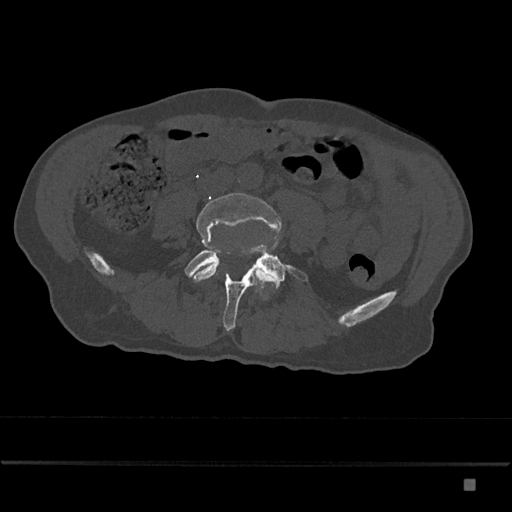
CT including the spine, one axial slice. Position 304 of 797 along the scan axis. Reconstruction kernel Br40s/3. Bone window (W 1800 / L 400 HU). 0.5 mm slice thickness. 512 × 512 image matrix, field of view 390 × 390 mm. Male patient, age 72 years. From the clinical record (not read from this slice): primary cancer: prostate.
Structures marked on this image (semi-automatically segmented with operator editing):
- L4 vertebra: bounding box <190,193,282,282> (left, top, right, bottom; pixels)
- L5 vertebra: <185,247,308,331>